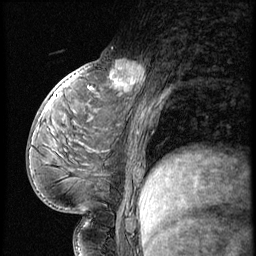
Breast MRI (dynamic contrast-enhanced), one sagittal slice; position 28 of 56 along the scan axis; 3 images stored at this slice position (order not interpretable as contrast timing); 1.5 T; TE 4.2 ms, TR 9 ms; 256 × 256 image matrix. Patient: female, 54 years. From the clinical record (not read from this slice): setting: breast cancer imaged before/during neoadjuvant chemotherapy; receptor status: triple-negative.
Structures marked on this image (semi-automatically segmented with operator editing):
- analysis volume of interest (the breast-tissue region the enhancement analysis was run in; not a lesion): bounding box (x1, y1, x2, y2) in pixels: (99, 53, 149, 102)
- tumour enhancement mask (voxels above the 140 % enhancement threshold inside the analysis volume of interest): (110, 60, 145, 91)